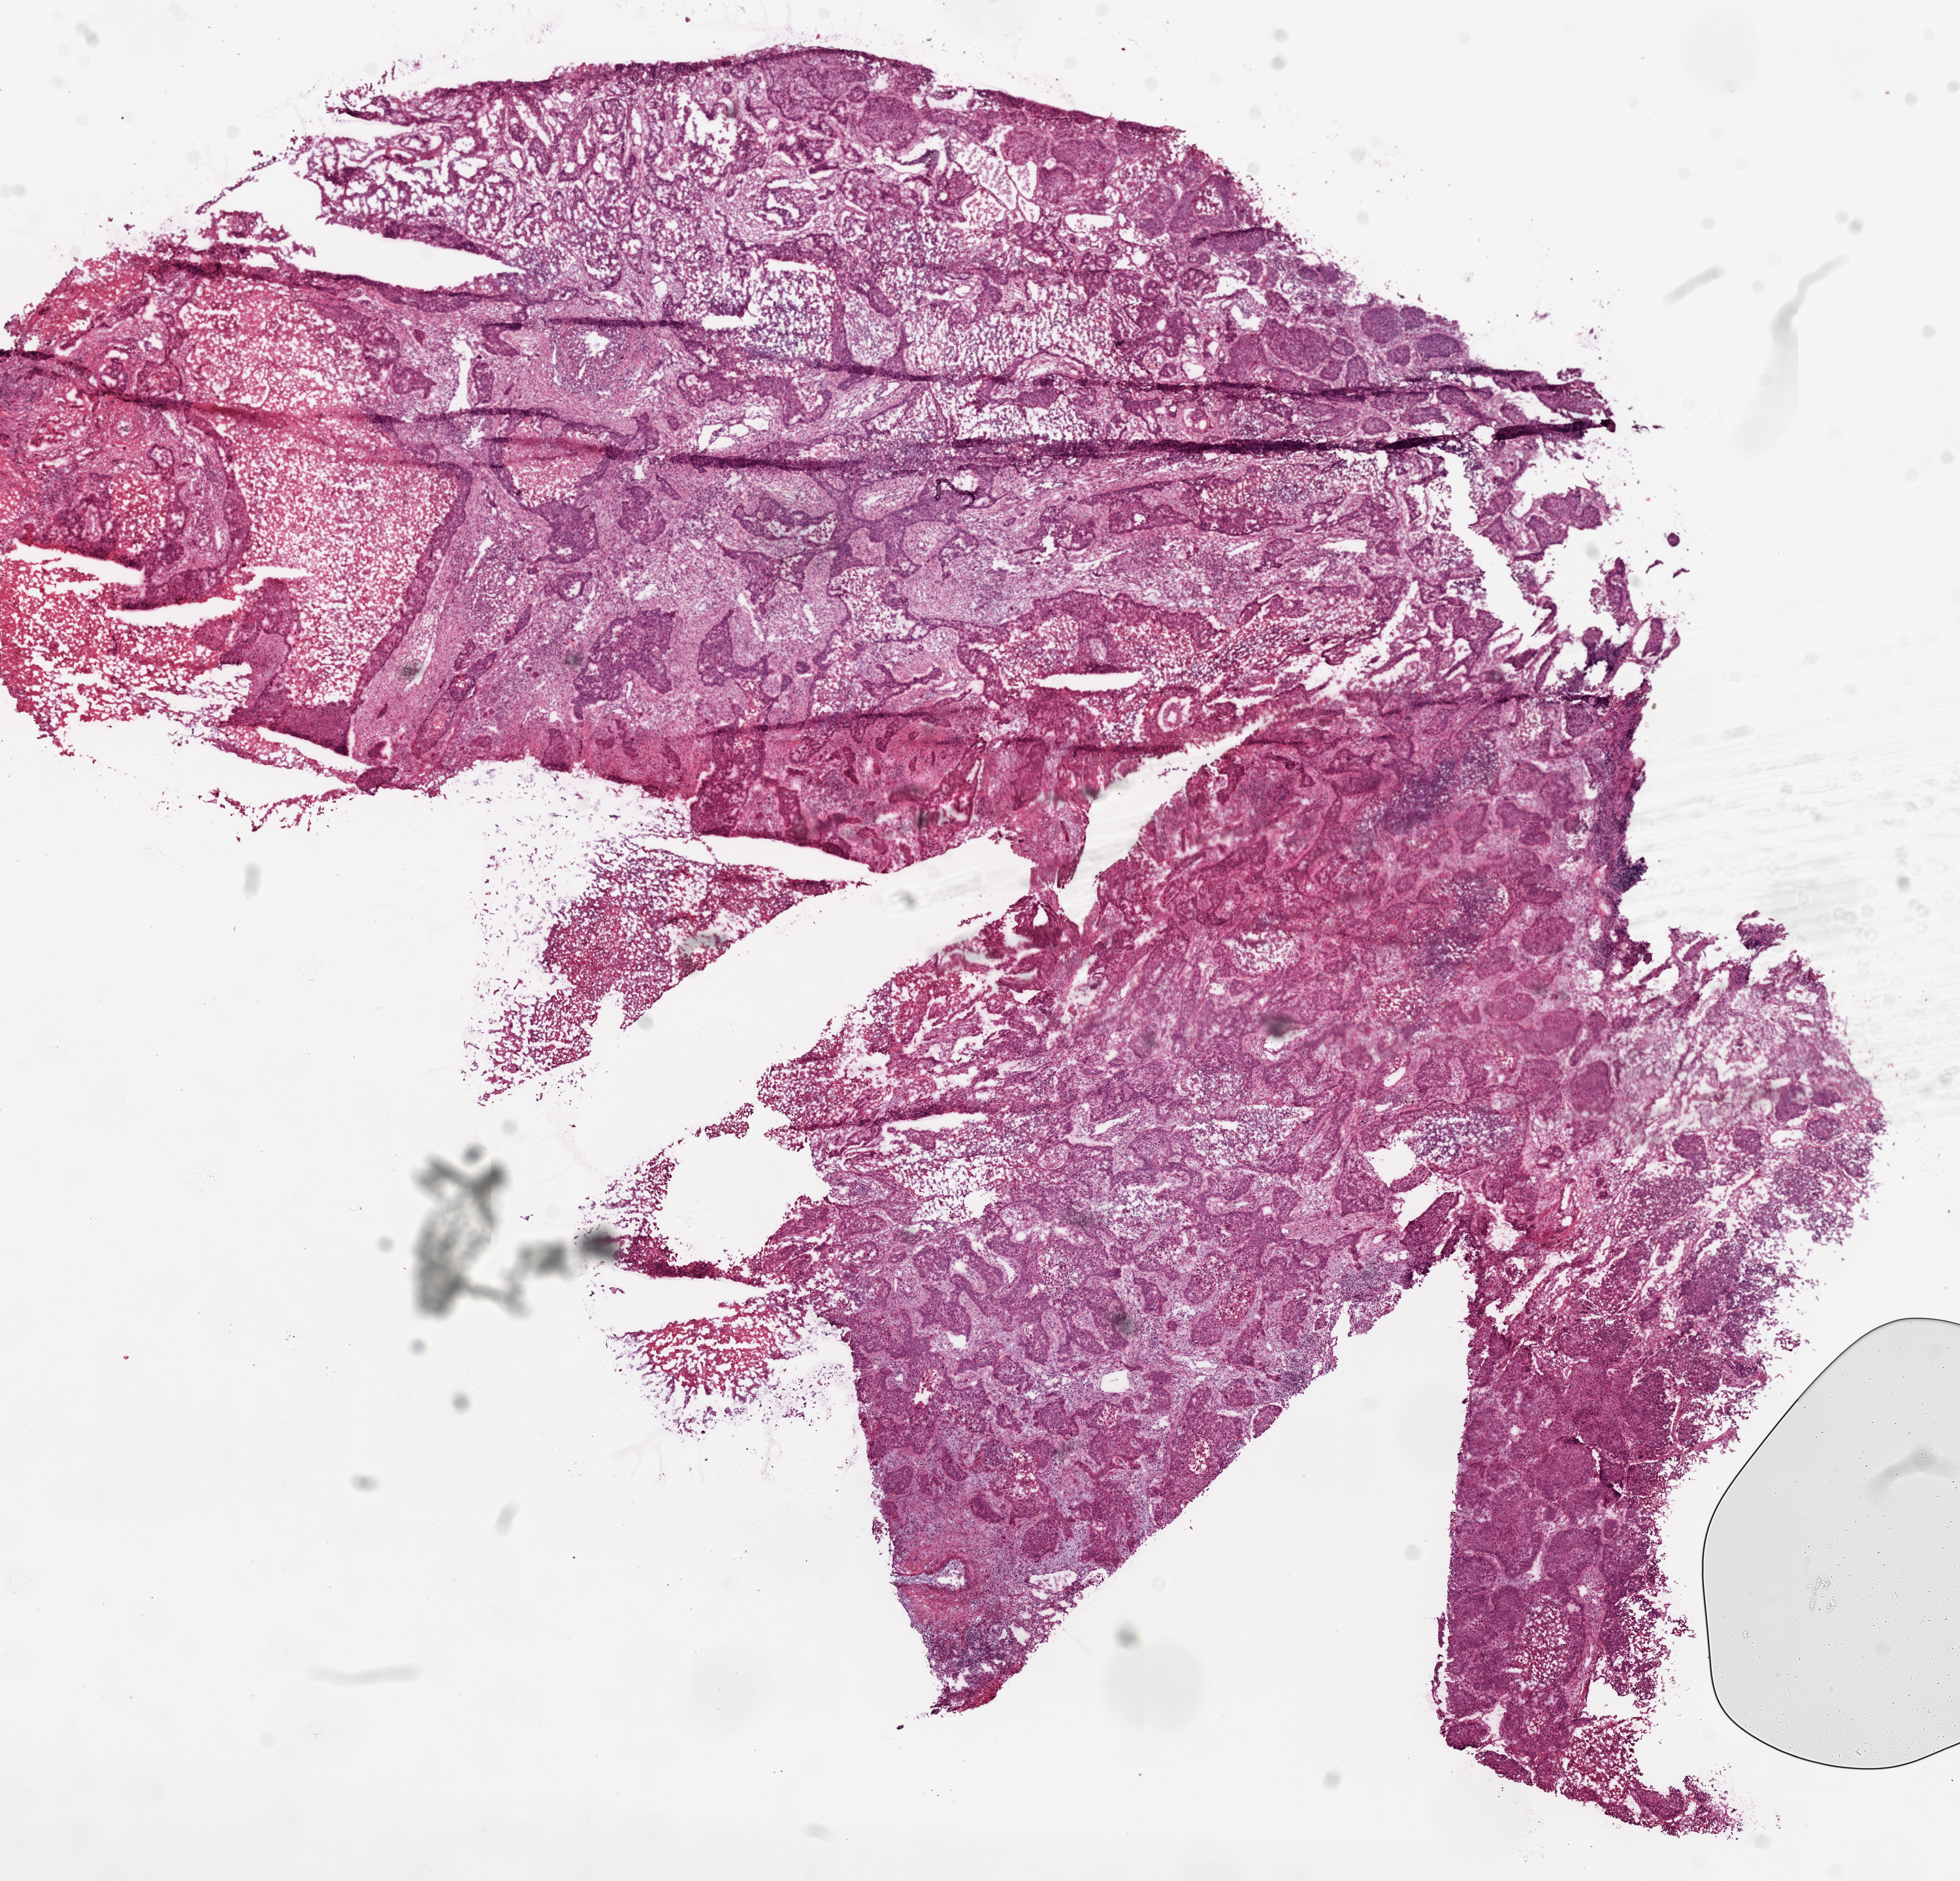
Digitized H&E tissue section (whole slide), shown as a low-resolution overview of the whole scanned area (about 12.0 x 11.6 mm), frozen section from the top of the tissue portion, primary tumour sample from the lung. Male patient; age at initial diagnosis 57 years. Composition of this section per pathologist review: tumour cells 65%, tumour nuclei 65%, normal cells 0%, stromal cells 20%, necrosis 15%.
AJCC pathologic stage: IIIA. Laterality: left. Histologic diagnosis: Squamous cell carcinoma, NOS (lower lobe, lung).